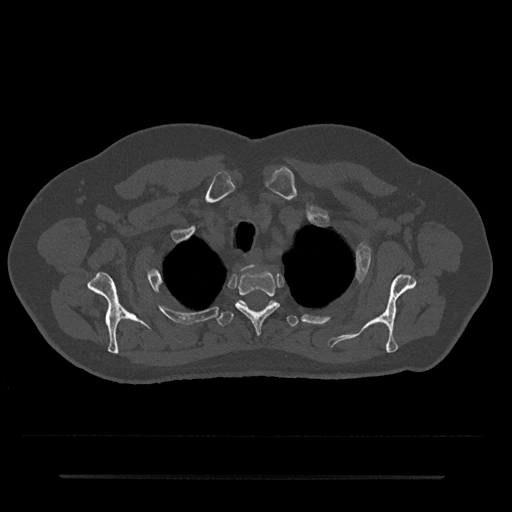
CT including the spine, one axial slice; slice 597 of 797 in the series (ordered by position); 120 kVp; bone window (W 1800 / L 400 HU); 0.5 mm slice thickness; 512 × 512 image matrix, field of view 437 × 437 mm. Patient: male, 69 years. Case-level facts recorded for this patient, not image findings: primary cancer: prostate.
Structures marked on this image (semi-automatically segmented with operator editing):
- T1 vertebra: box from (x=243, y=265) to (x=252, y=271) px
- T2 vertebra: (x=235, y=270)–(x=279, y=334)
- T3 vertebra: (x=217, y=300)–(x=298, y=327)